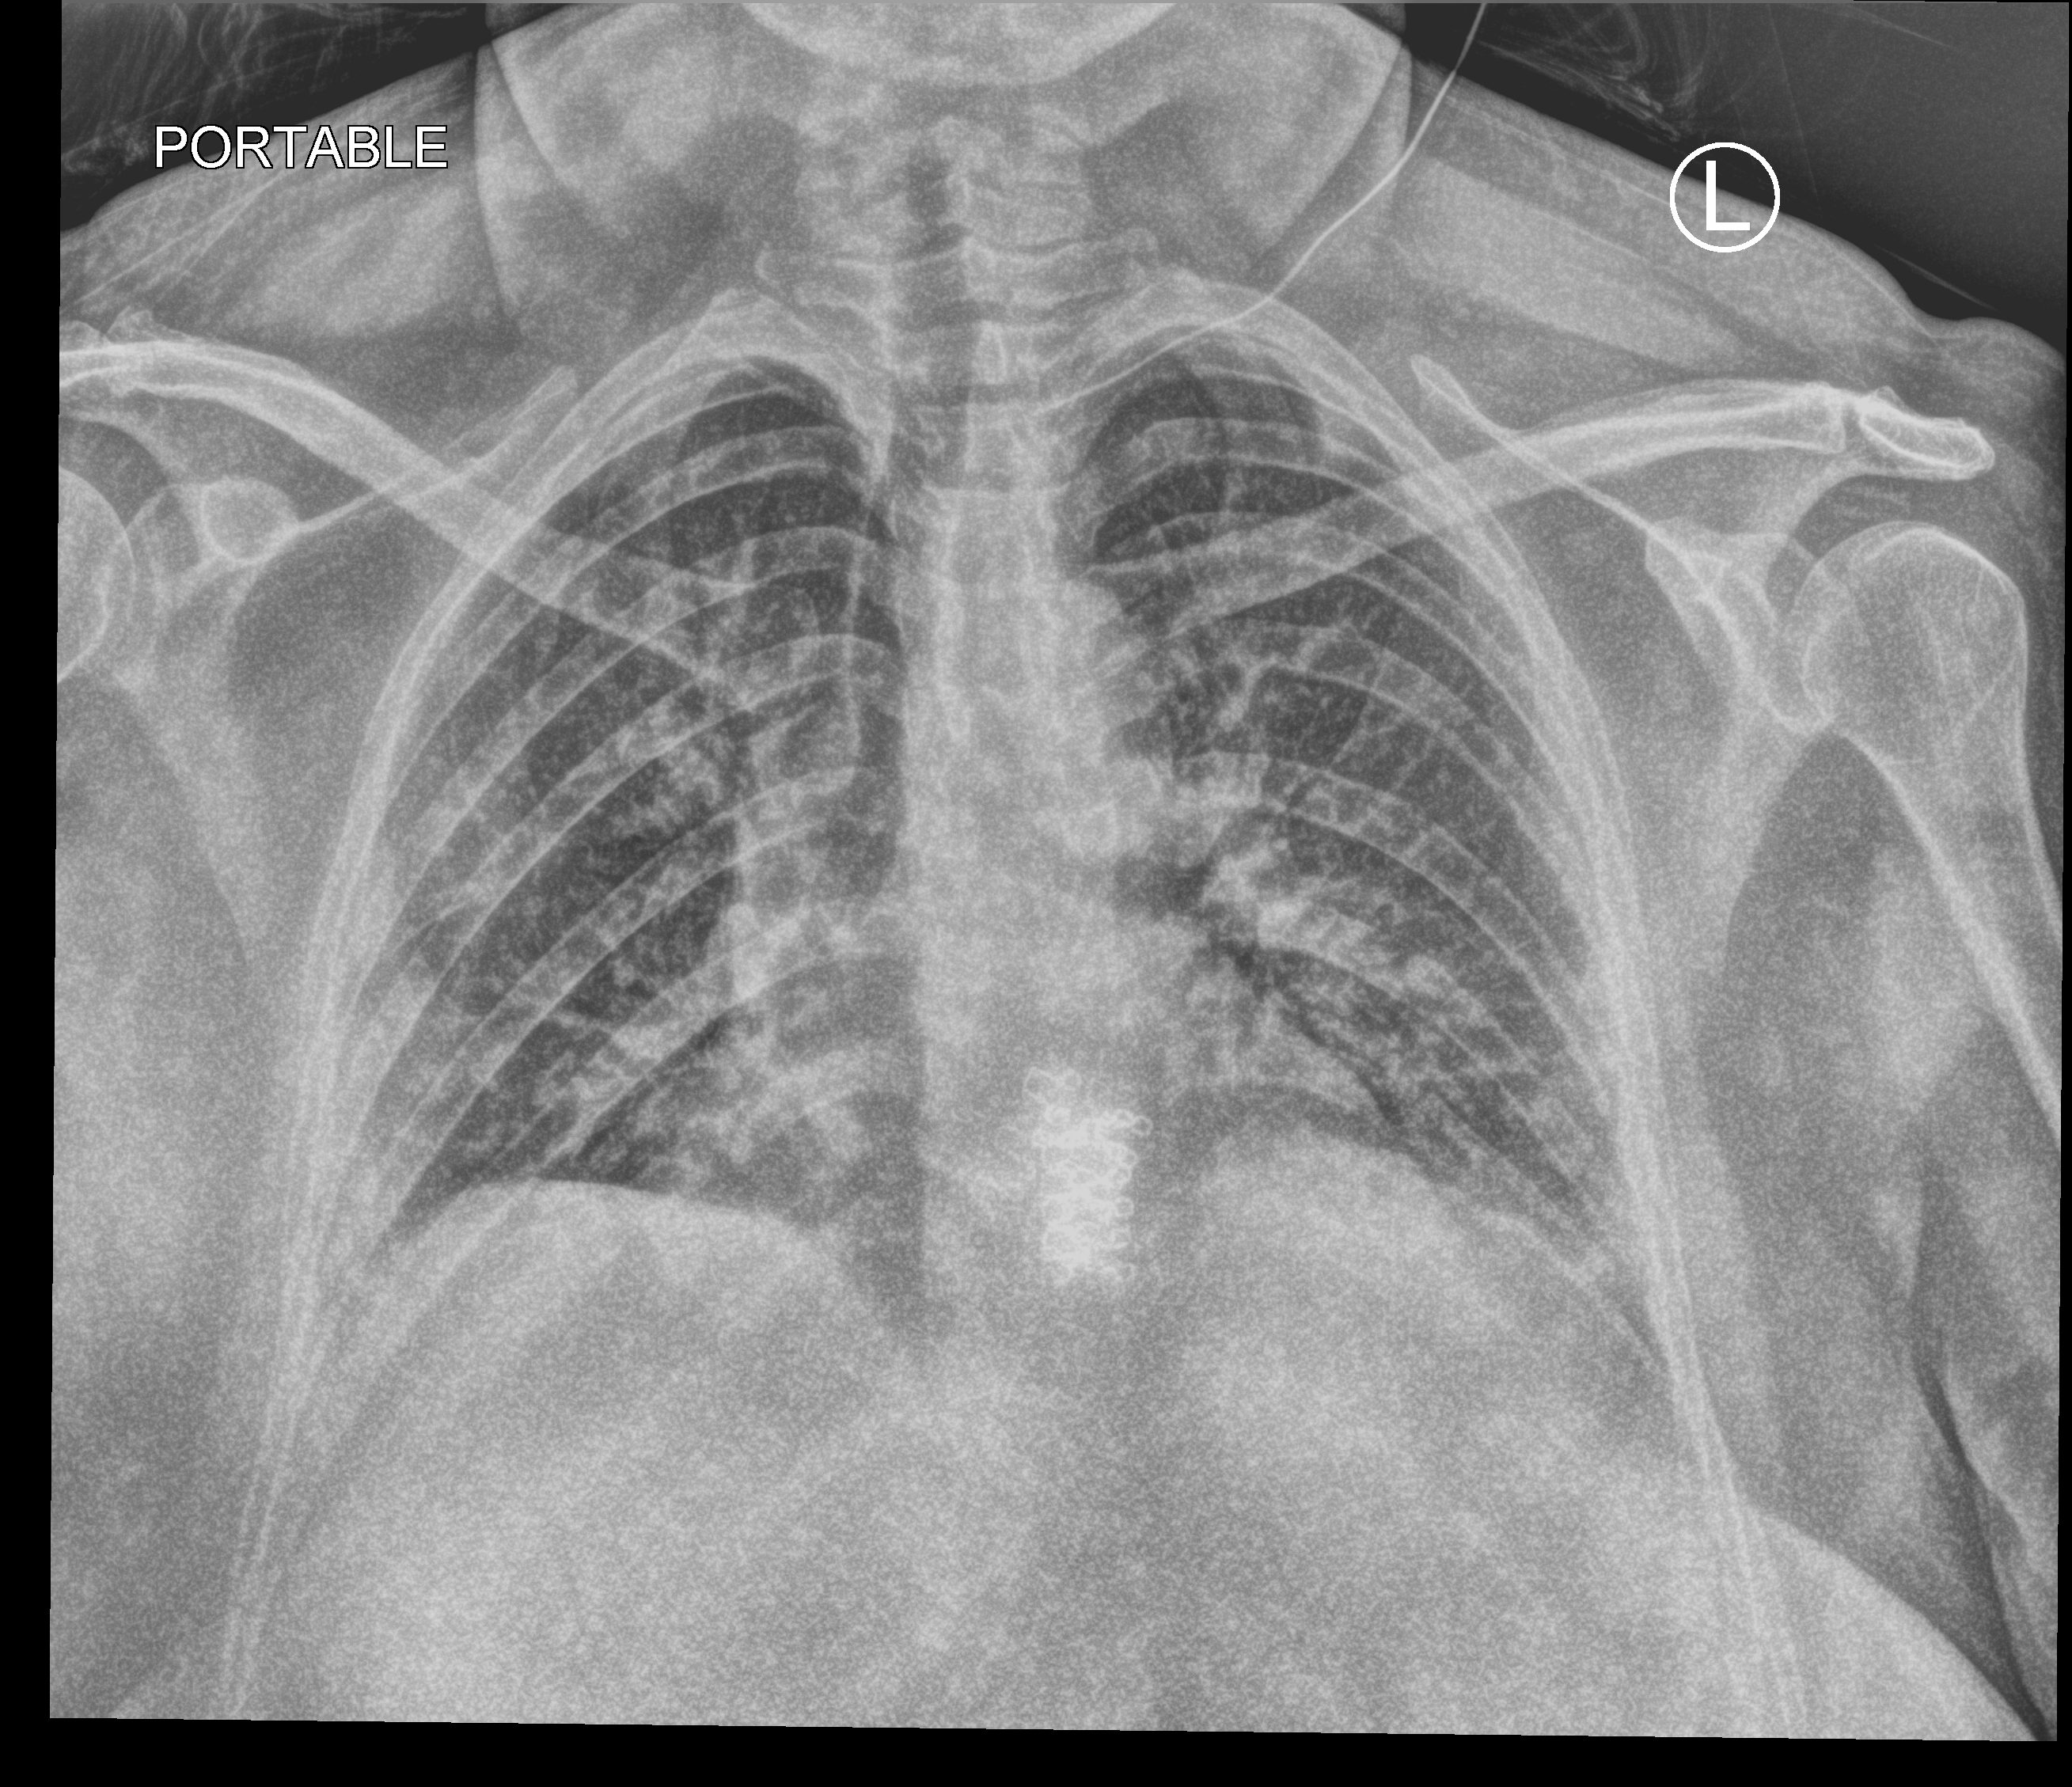
Bedside chest radiograph (computed radiography). Patient hospitalised with COVID-19; female, aged 18–59 years.
From the hospital-stay record, not from the radiograph (when in the stay this image was taken is not recorded): diabetes (admission record): yes; mechanically ventilated during this hospital stay: no; other chronic lung disease (admission record): no.